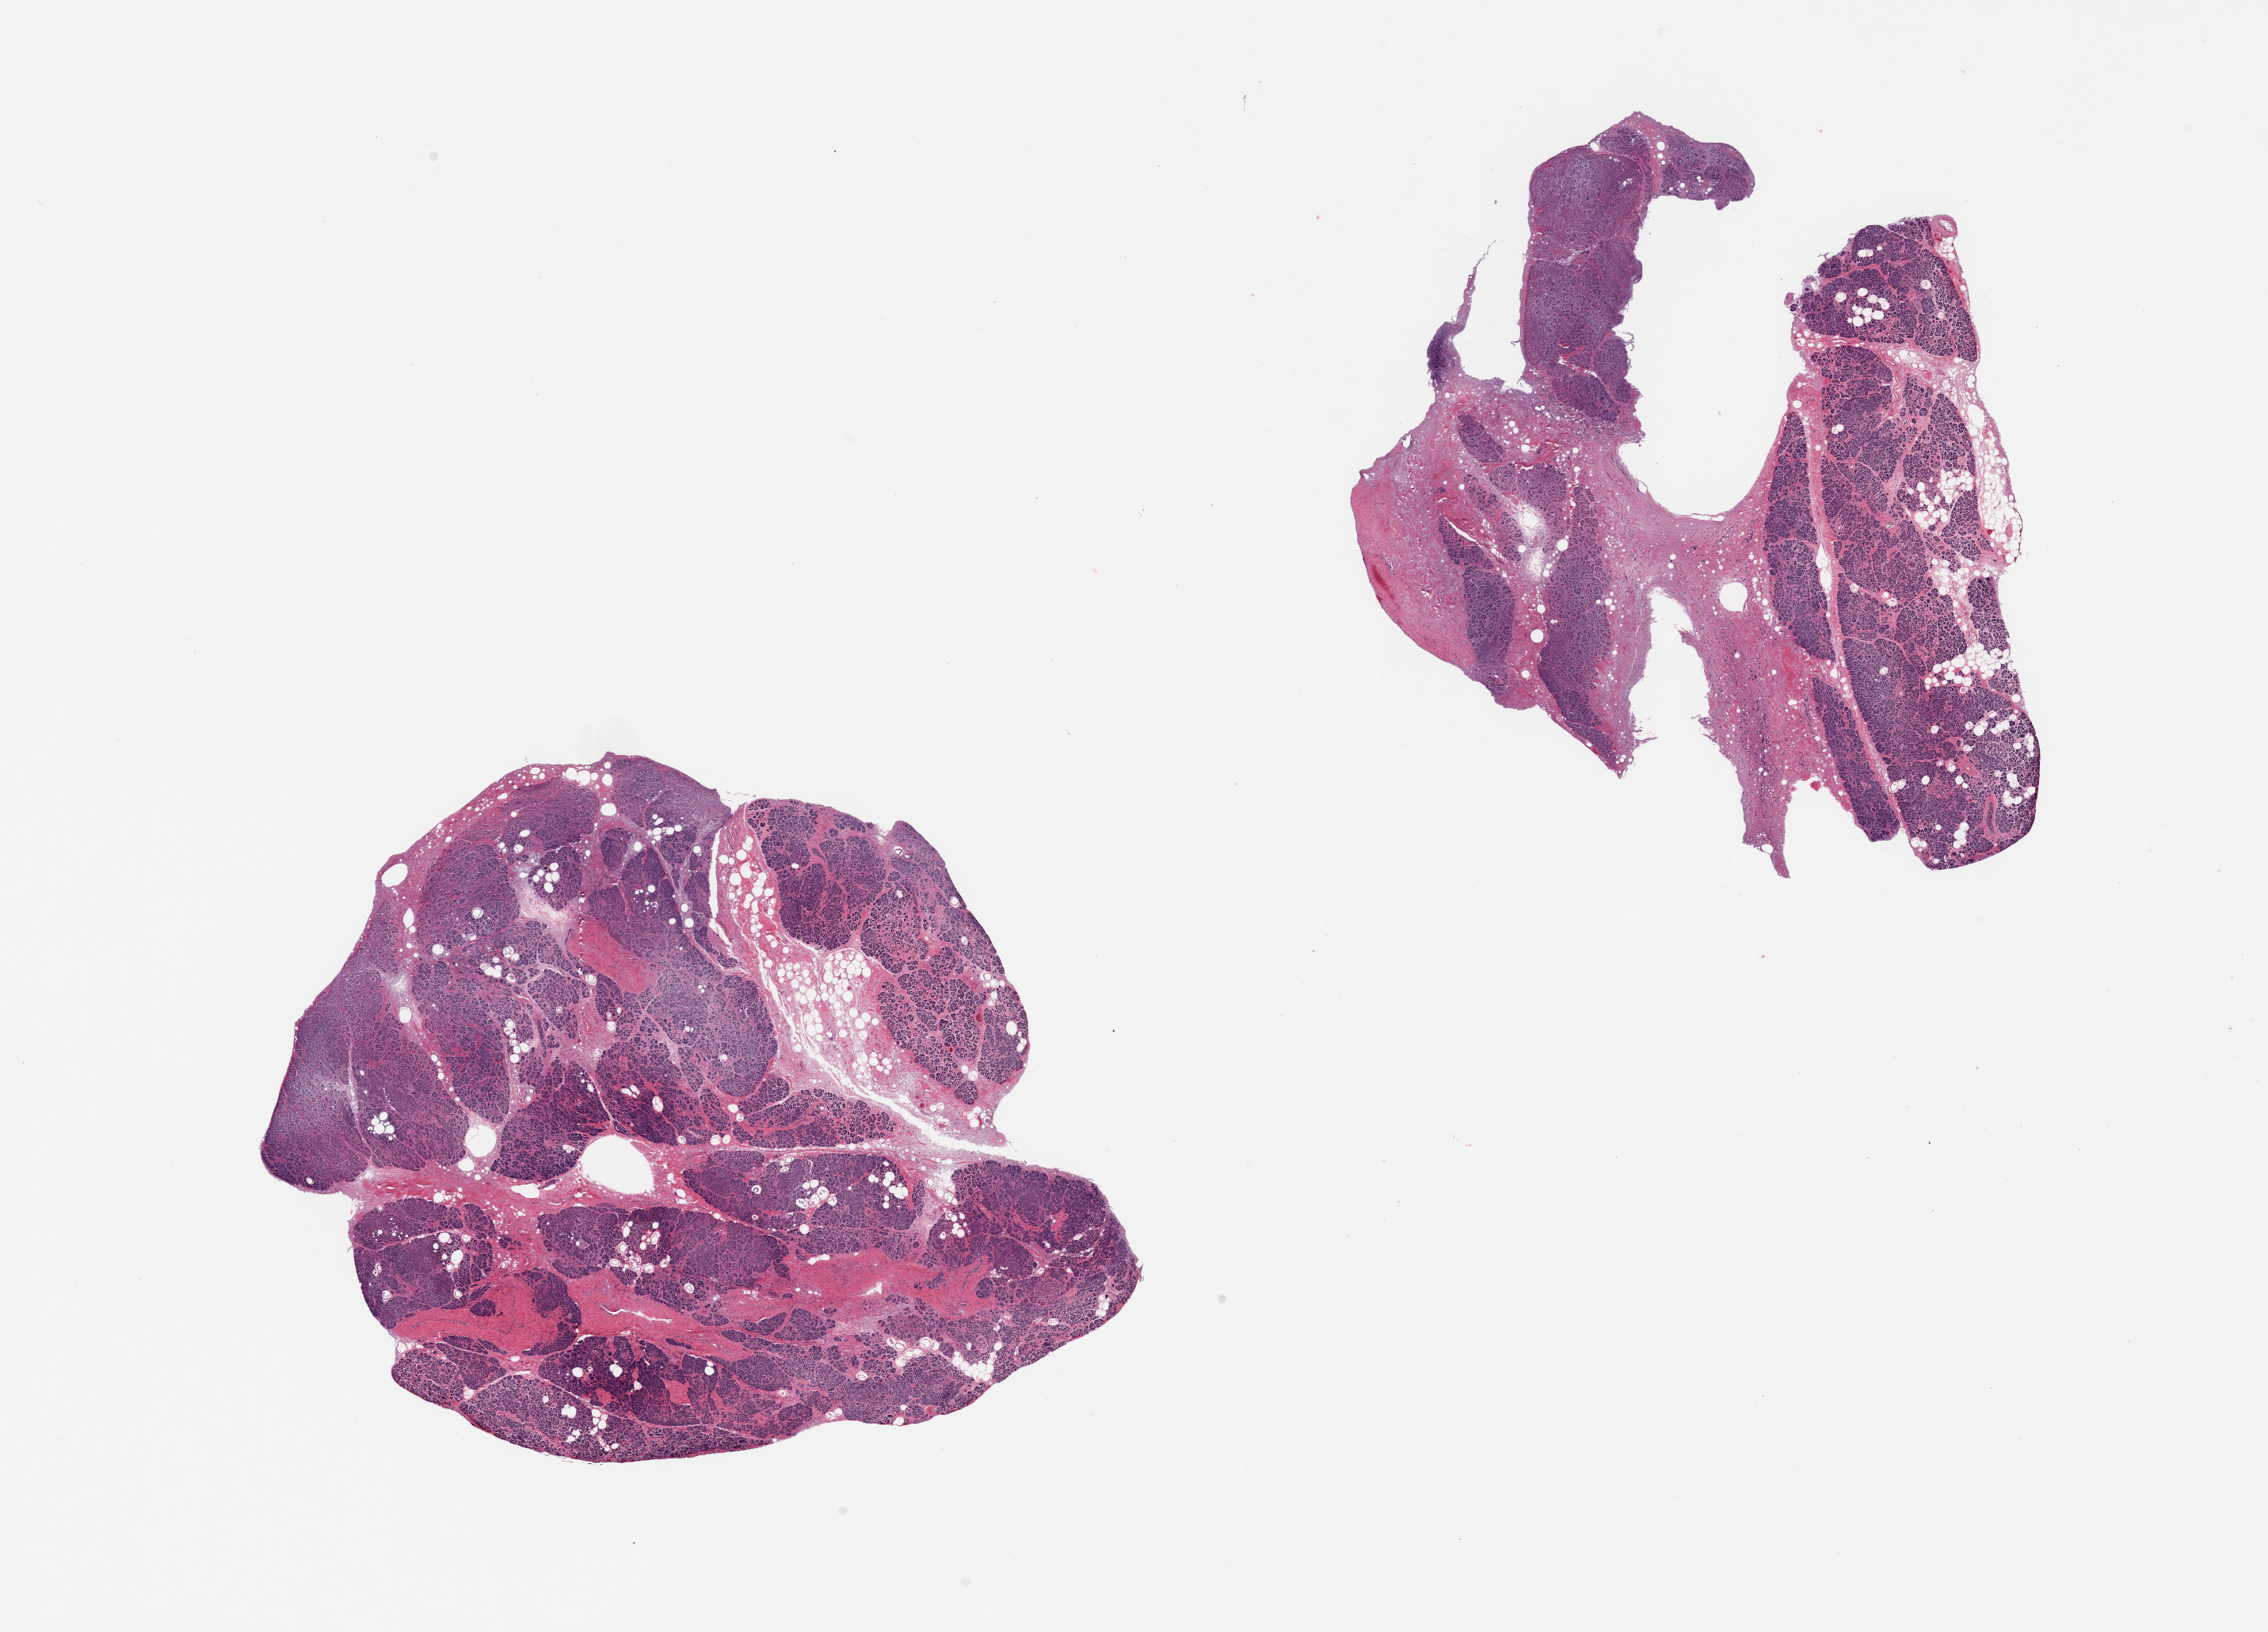
Whole-slide image, haematoxylin and eosin stain, shown as a low-resolution overview of the whole scanned area (about 22.6 x 16.3 mm). PAXgene-fixed, paraffin-embedded tissue. Target tissue: pancreas. Tissue donor sample.
Reviewer comment on this tissue sample: 2 pieces; too autolyzed.